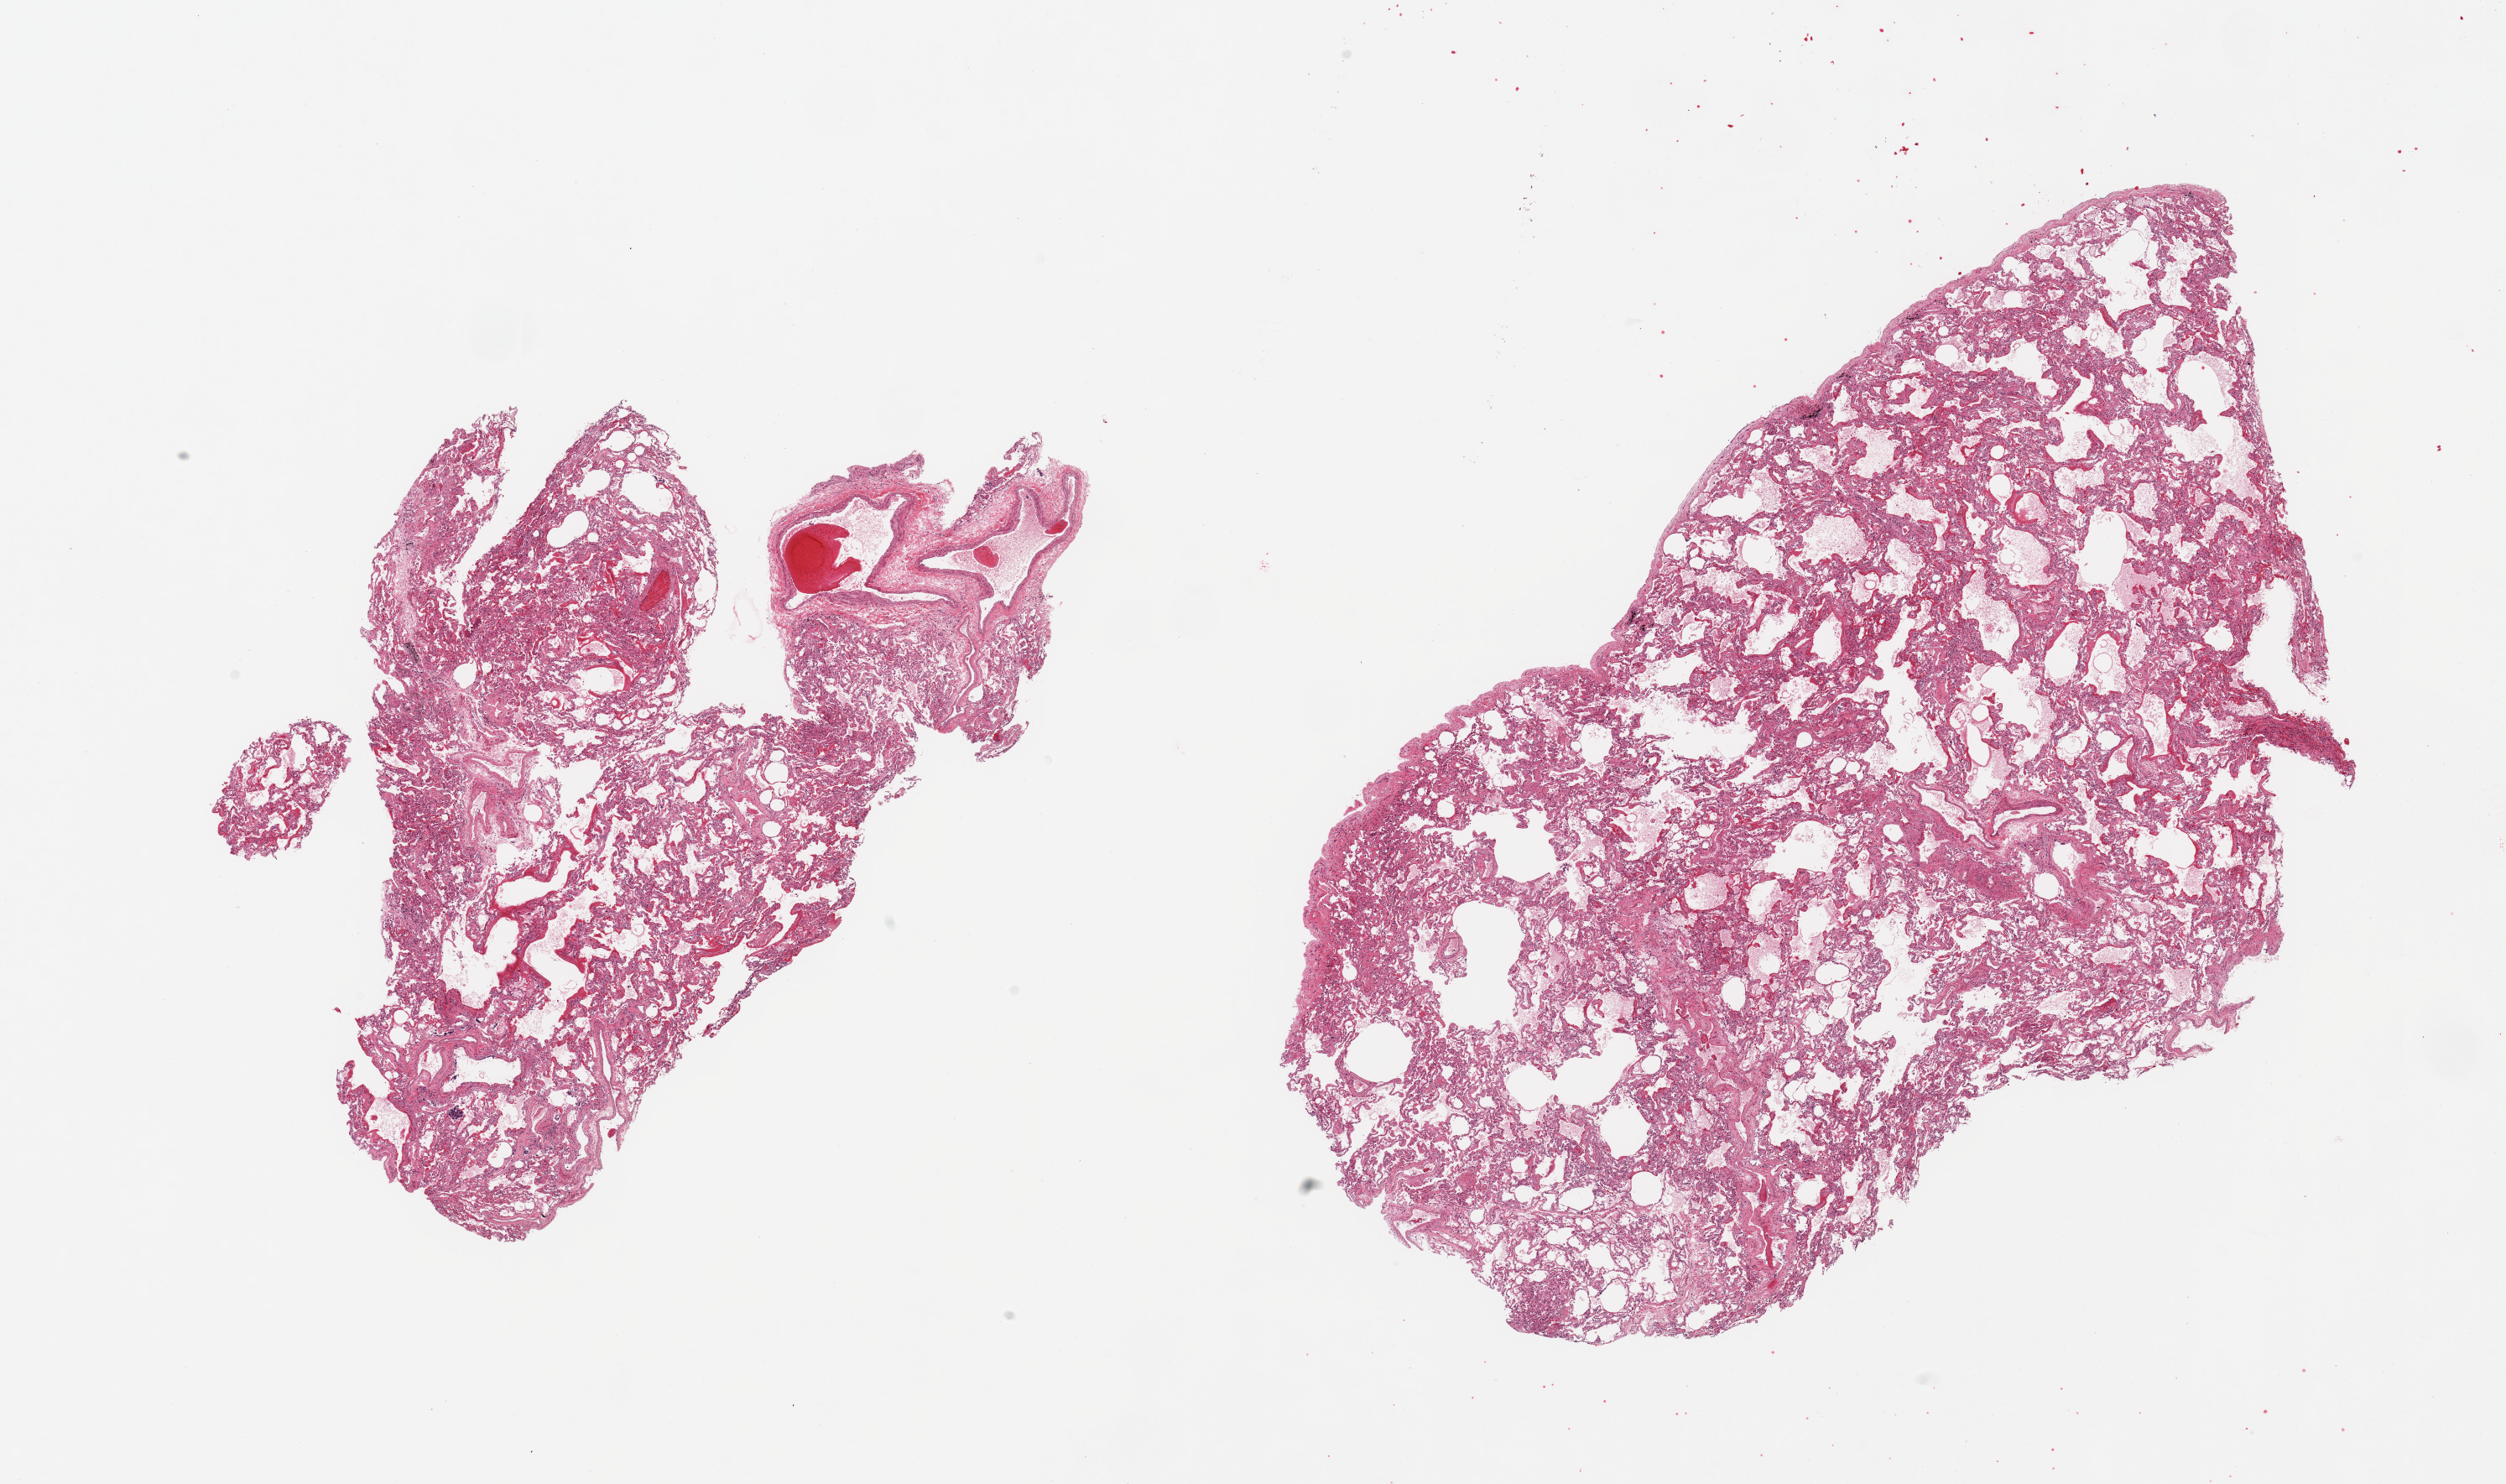
Whole-slide image, haematoxylin and eosin stain, a low-resolution overview of the entire scanned area, about 23.6 x 14.0 mm, PAXgene-fixed, paraffin-embedded tissue, target tissue: lung, tissue donor sample. Donor: female.
• review note (as recorded): 2 pieces; pulmonary edema; early patchy bronchopneumonia